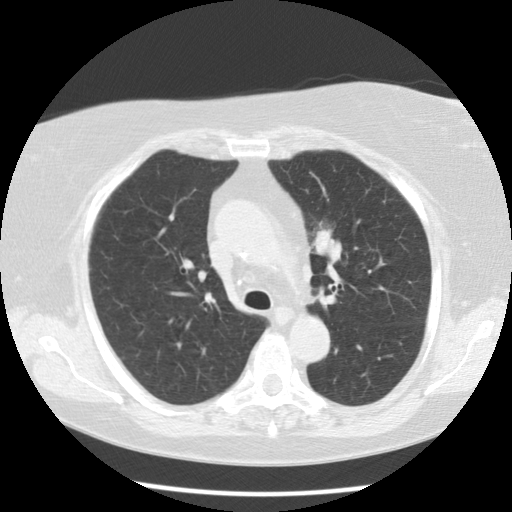
Axial slice from a low-dose chest CT screening exam. Second screening round (one year after baseline). Lung window (W 1500 / L -600 HU). Female, age 67 years at enrolment.
Lesion marked by an expert reader, box from (x=292, y=211) to (x=352, y=270) px. The exam's reader record, not a measurement of the box and not confirmed to be the same lesion: non-calcified nodule or mass ≥4 mm, left upper lobe, 20 × 18 mm, poorly defined margins, soft tissue attenuation, pre-existing on the prior screen: yes; interval growth: yes. Later outcome: lung cancer diagnosed 28 days after this screen — adenocarcinoma, NOS, left upper lobe, moderately differentiated (G2), stage IIA (AJCC 6th edition), 23 mm at pathology.